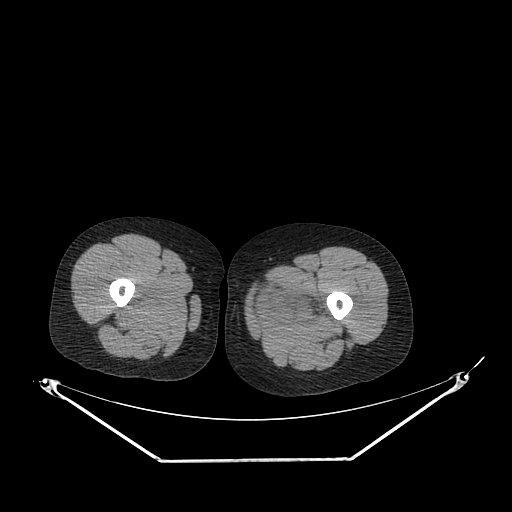
CT of an extremity soft-tissue mass (from a PET/CT study), one axial slice. Position 226 of 267 along the scan axis. 120 kVp. Soft-tissue window (W 400 / L 40 HU). 3.75 mm slice thickness. 512 × 512 image matrix. Female patient. From the clinical record (not read from this slice): histological type: pleiomorphic leiomyosarcoma; grade: intermediate; site of the primary tumour: left thigh.
Structures marked on this image (expert contour drawn on MRI and transferred to this co-registered scan by the dataset authors):
- gross tumour volume including surrounding oedema: bounding box [x1, y1, x2, y2] px = [254, 279, 323, 321]